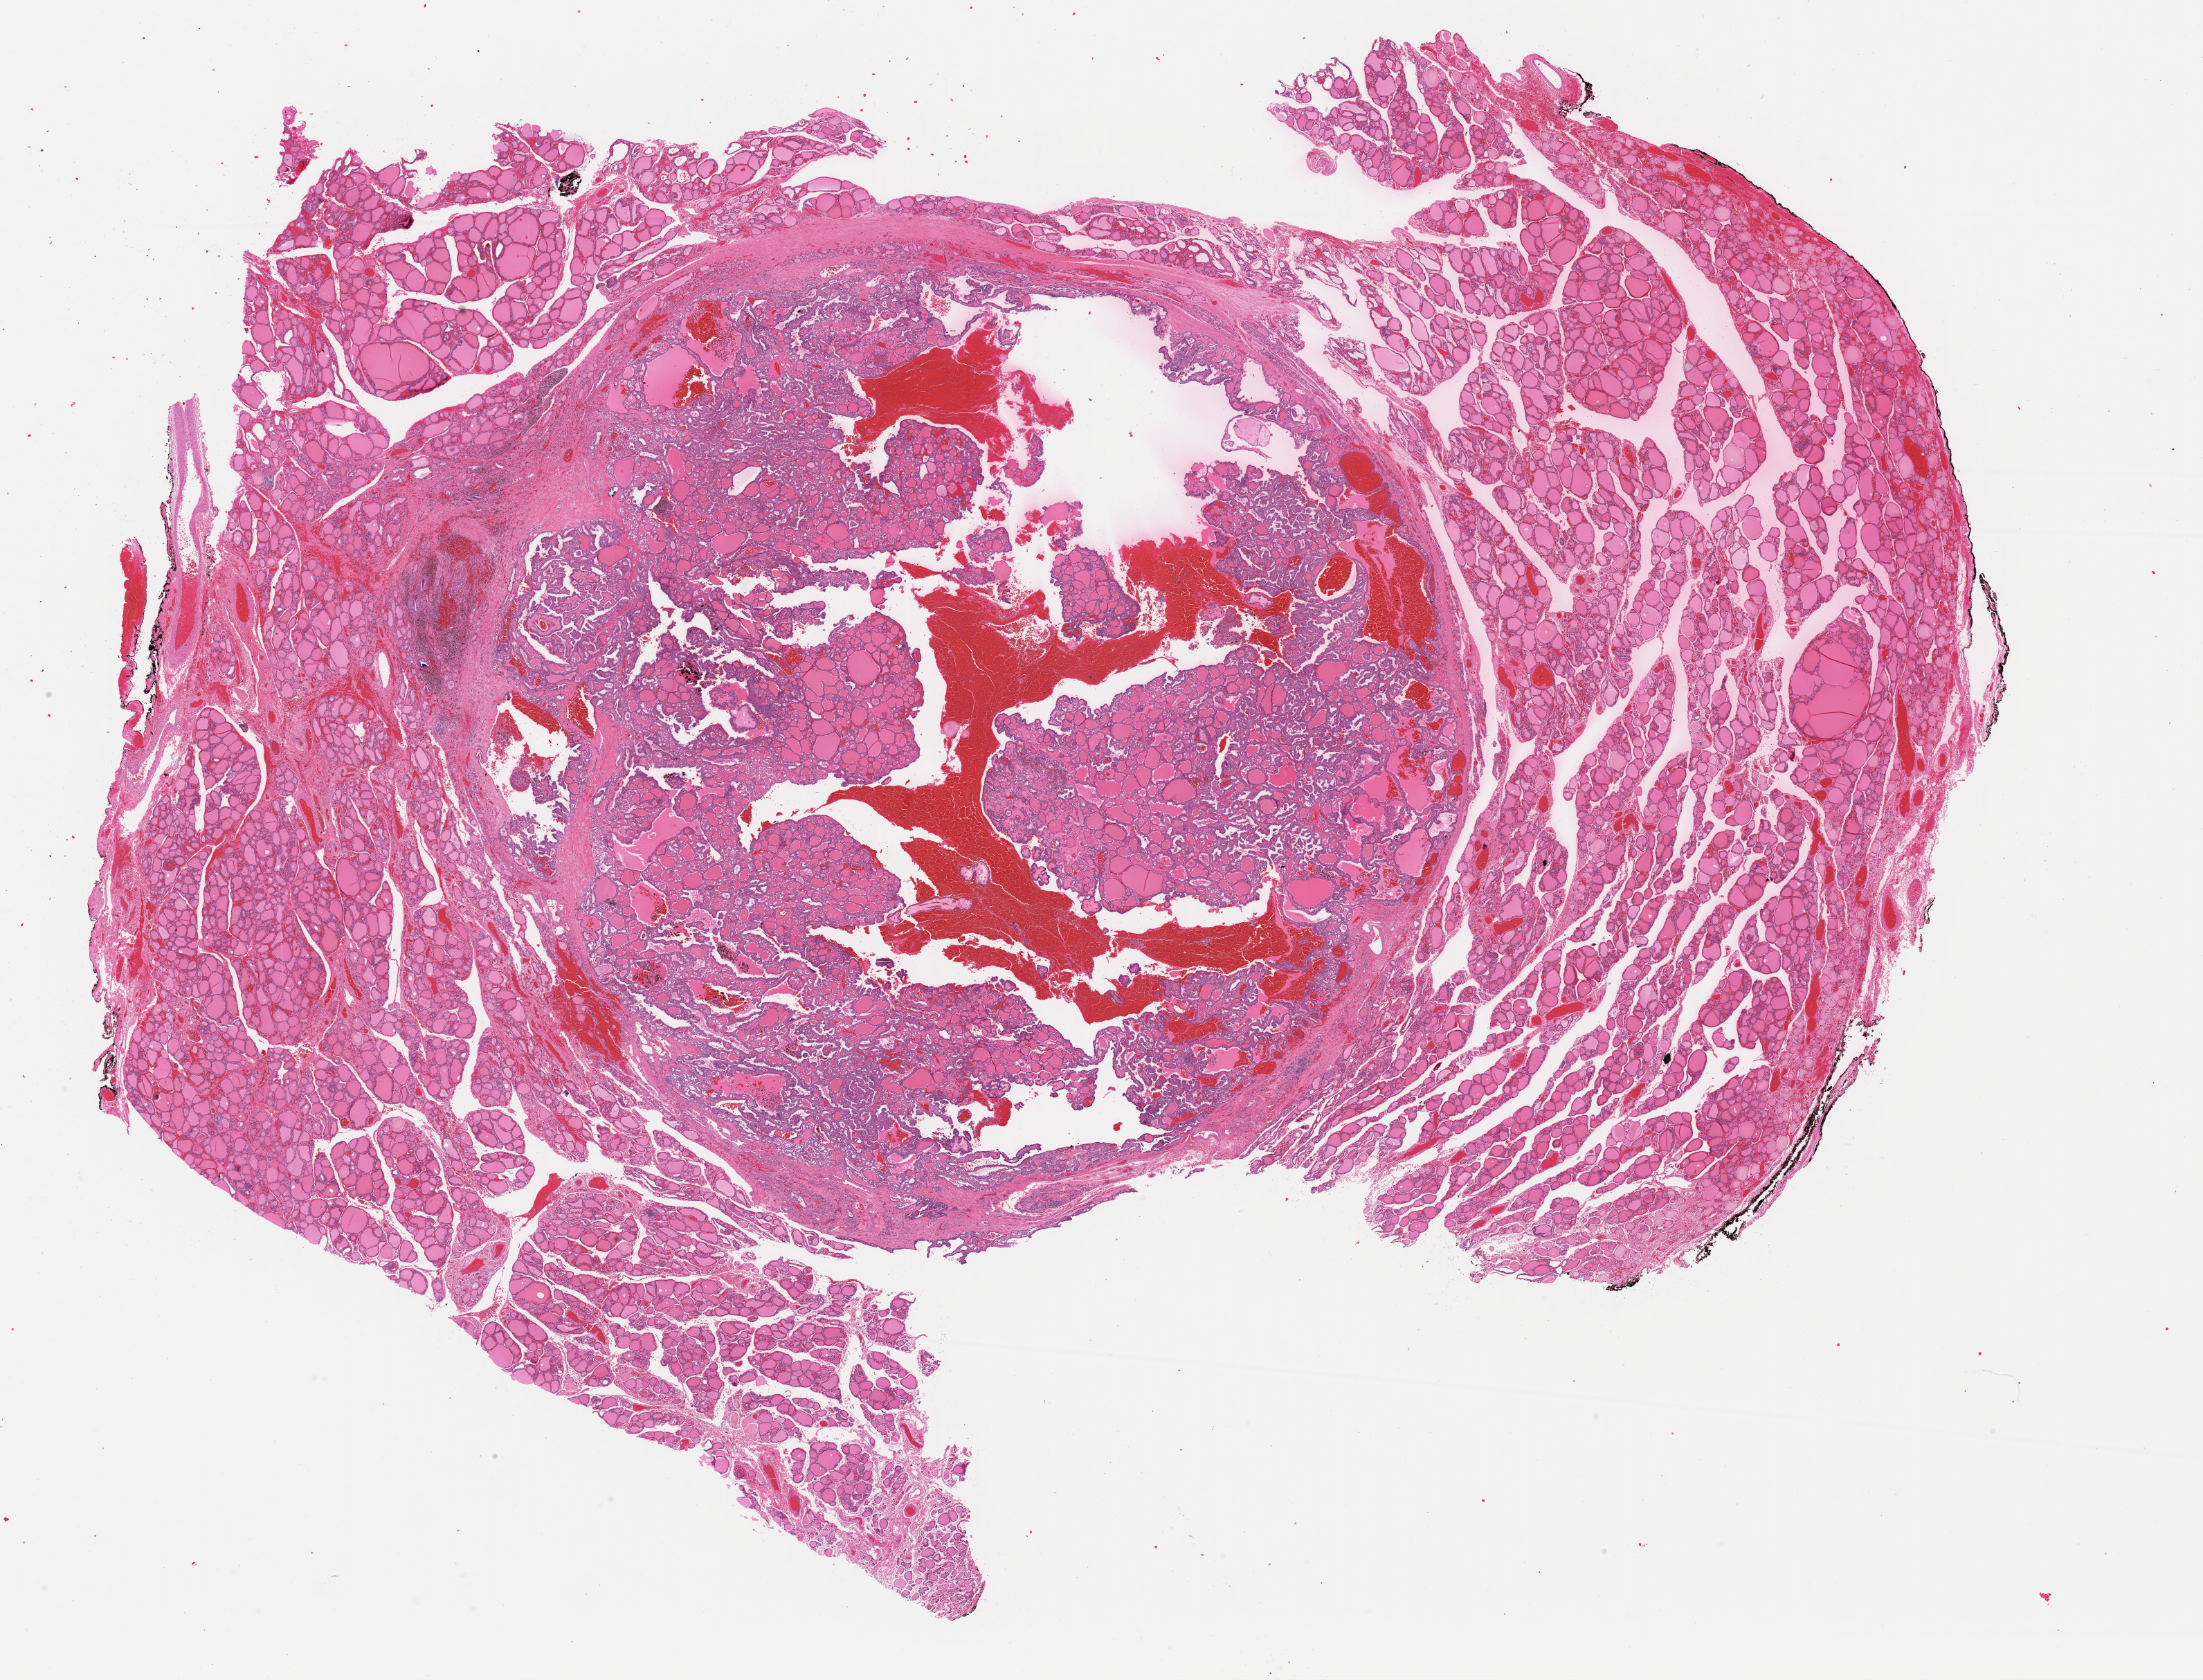
Digitized Hematoxylin and eosin (H&E) stained tissue section (whole slide), a low-resolution overview of the entire scanned area, about 25.1 x 19.2 mm (acquisition: 40x scan), FFPE section, thyroid, primary tumour sample. Female patient; age at initial diagnosis 43 years.
TNM: T2 NX MX. Laterality: left. Histologic diagnosis: Papillary adenocarcinoma, NOS (thyroid gland). AJCC pathologic stage: I.